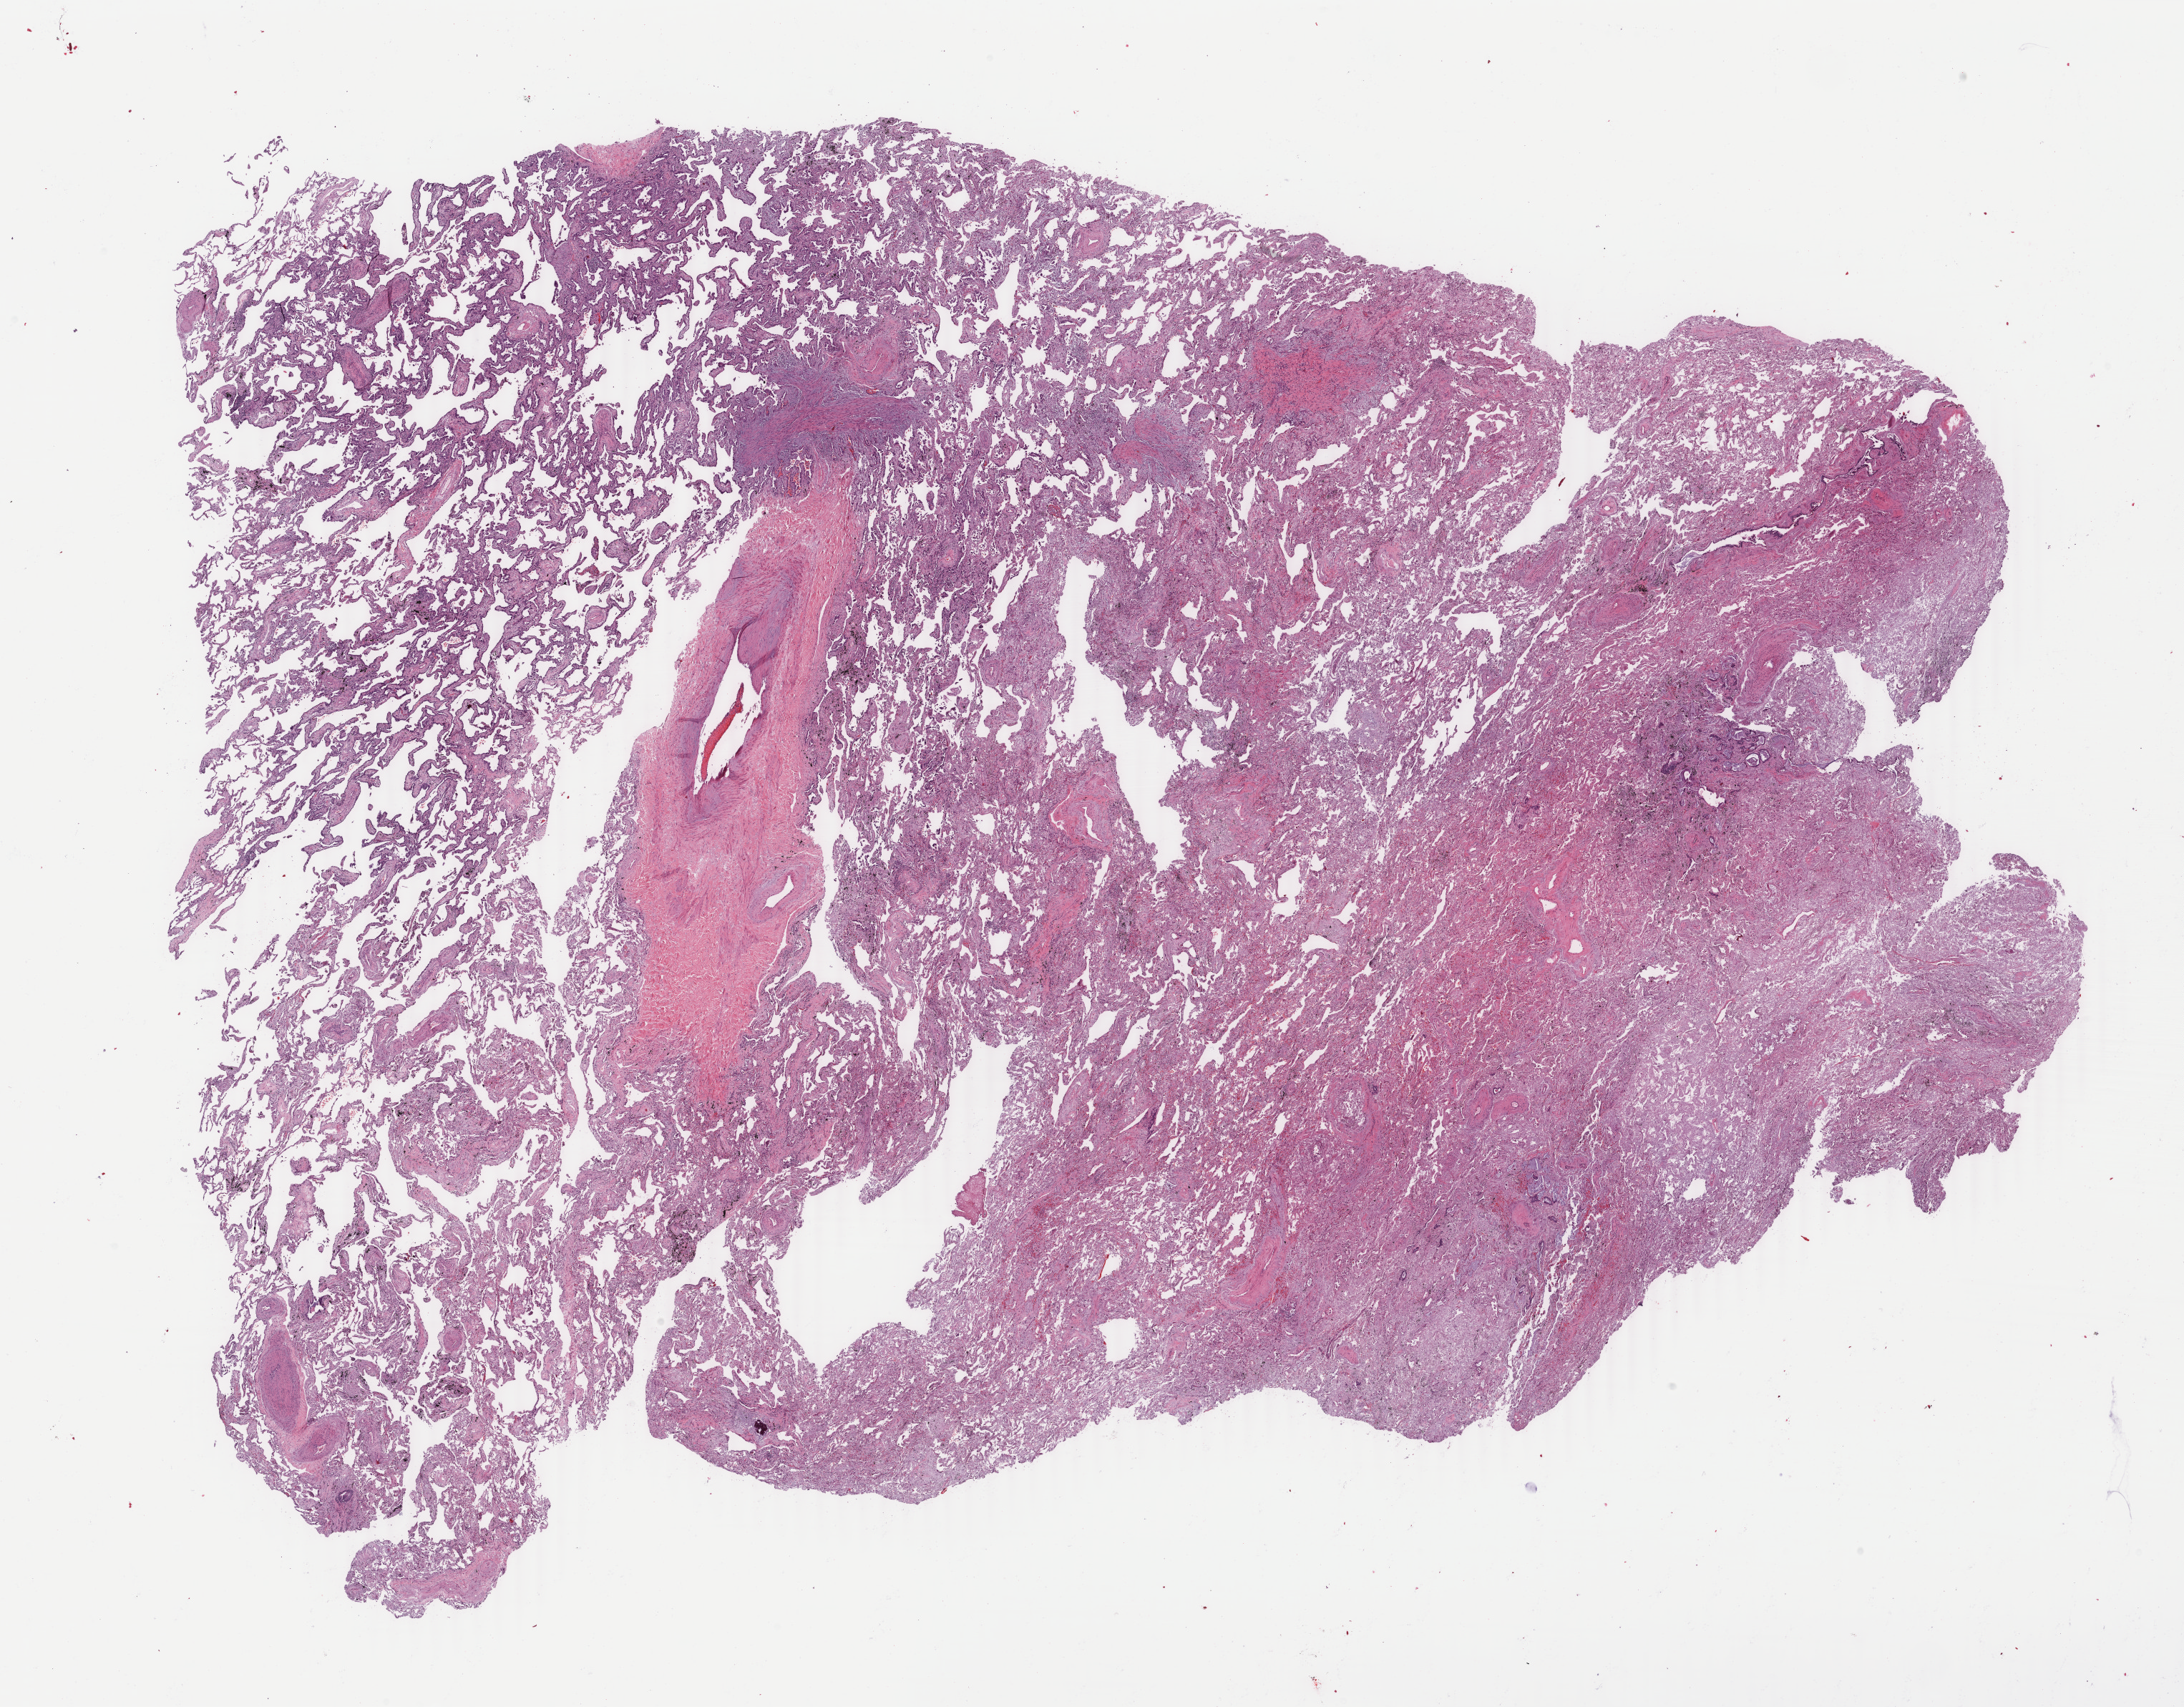
H&E-stained whole-slide image, whole scanned area (about 24.3 x 19.0 mm, acquisition: 40x scan) shown as a low-resolution overview; FFPE section; lung, primary tumour sample. Female, age 76 years at initial diagnosis.
Histologic diagnosis: Bronchiolo-alveolar carcinoma, non-mucinous (upper lobe, lung). AJCC pathologic stage: IA (7th edition).